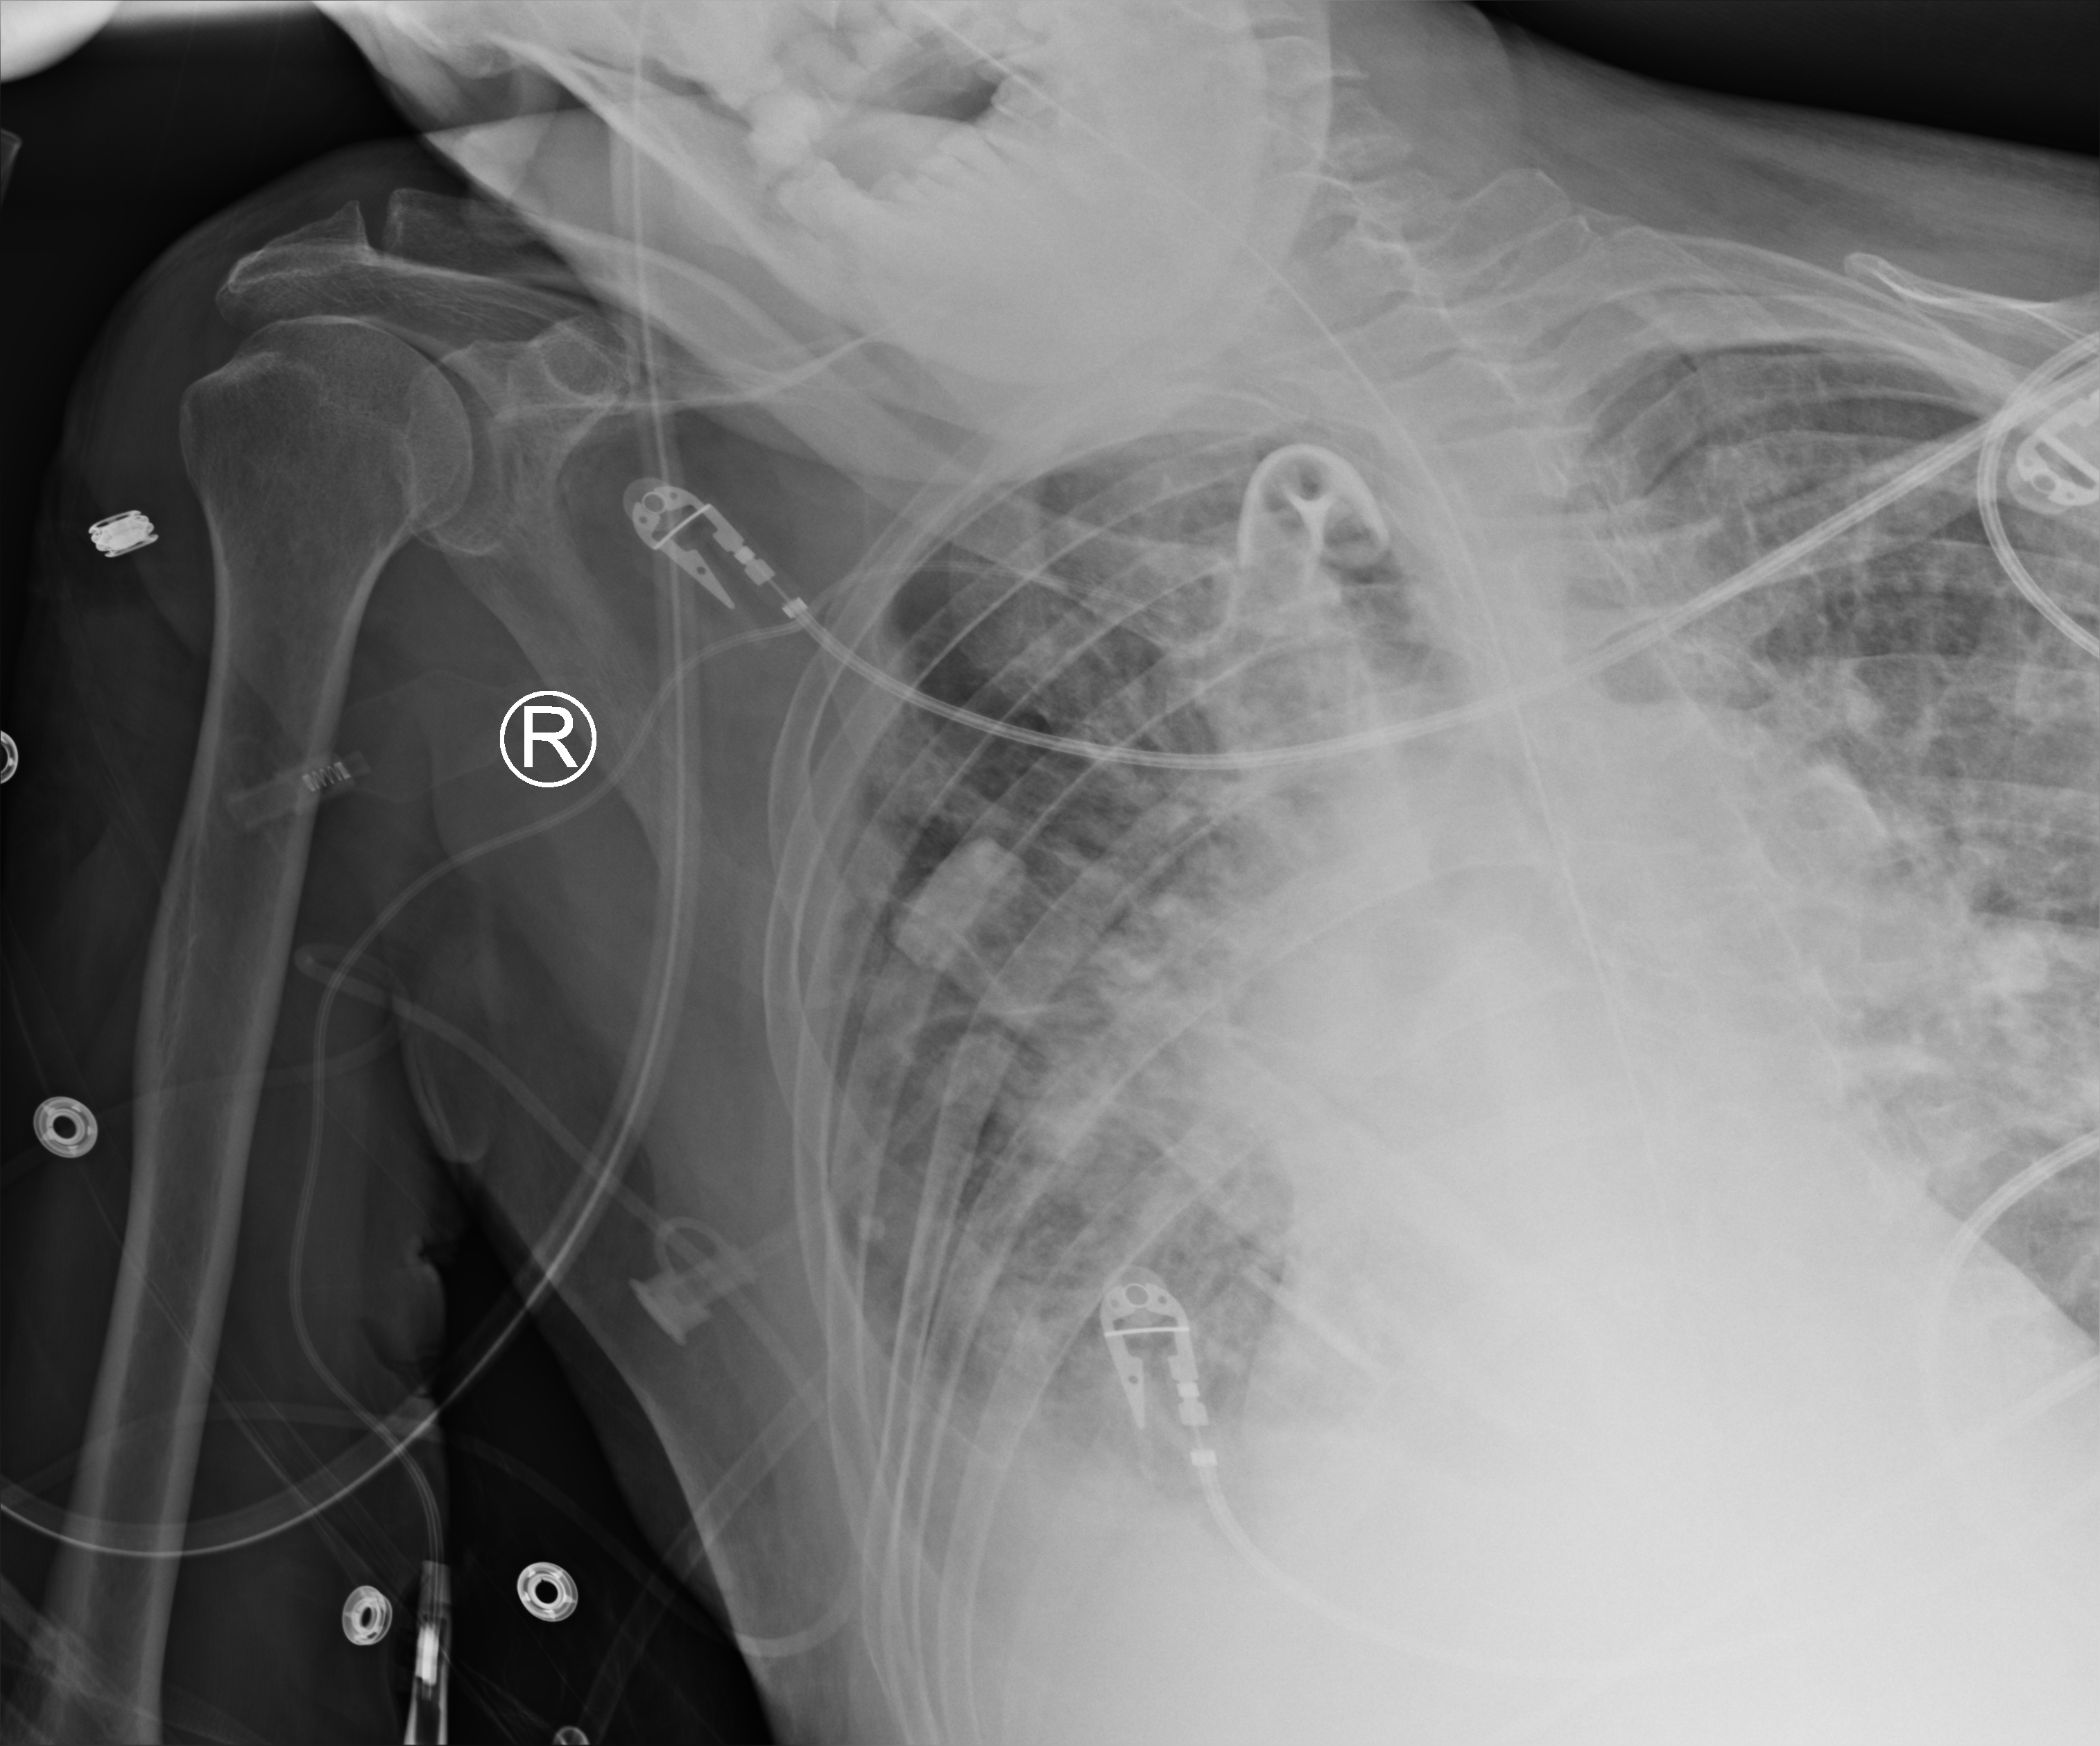
Chest X-ray (portable), anteroposterior (AP) projection. Patient hospitalised with COVID-19; male, aged 75–90 years.
Admission-level facts for this patient (not findings on this image; timing relative to this image not recorded): admitted to intensive care during this hospital stay: yes.